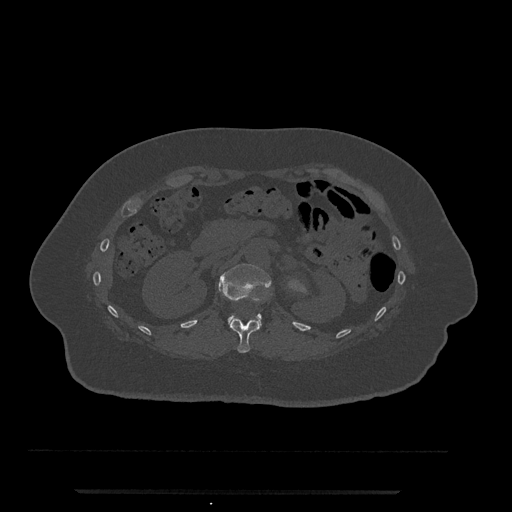
CT including the spine, one axial slice; position 138 of 797 along the scan axis; reconstruction kernel Br40s/3; 120 kVp; bone window (W 1800 / L 400 HU); 0.5 mm slice thickness; 512 × 512 image matrix, field of view 440 × 440 mm. Patient: female, 51 years. From the clinical record (not read from this slice): primary cancer: neuro; vertebrae with lytic lesions (as recorded): T8.
Outlined on this slice (semi-automatic segmentation, software-assisted and operator-edited):
- L1 vertebra: bounding box (x1, y1, x2, y2) in pixels: (218, 263, 271, 329)
- T12 vertebra: (230, 317, 259, 353)